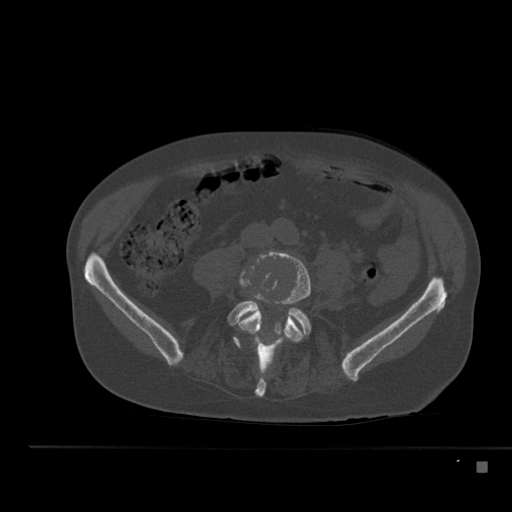
CT including the spine, one axial slice; position 135 of 517 along the scan axis; reconstruction kernel Br40s; 120 kVp; bone window (W 1800 / L 400 HU); 1.5 mm slice thickness; 512 × 512 image matrix, field of view 408 × 408 mm. Patient: male, 70 years. From the clinical record (not read from this slice): primary cancer: renal; vertebrae with lytic lesions (as recorded): T4, T6, T10, T12, L3, L4, L5.
Outlined on this slice (semi-automatically segmented with operator editing):
- L4 vertebra: bounding box (x1, y1, x2, y2) in pixels: (238, 251, 311, 369)
- L5 vertebra: (228, 301, 311, 396)